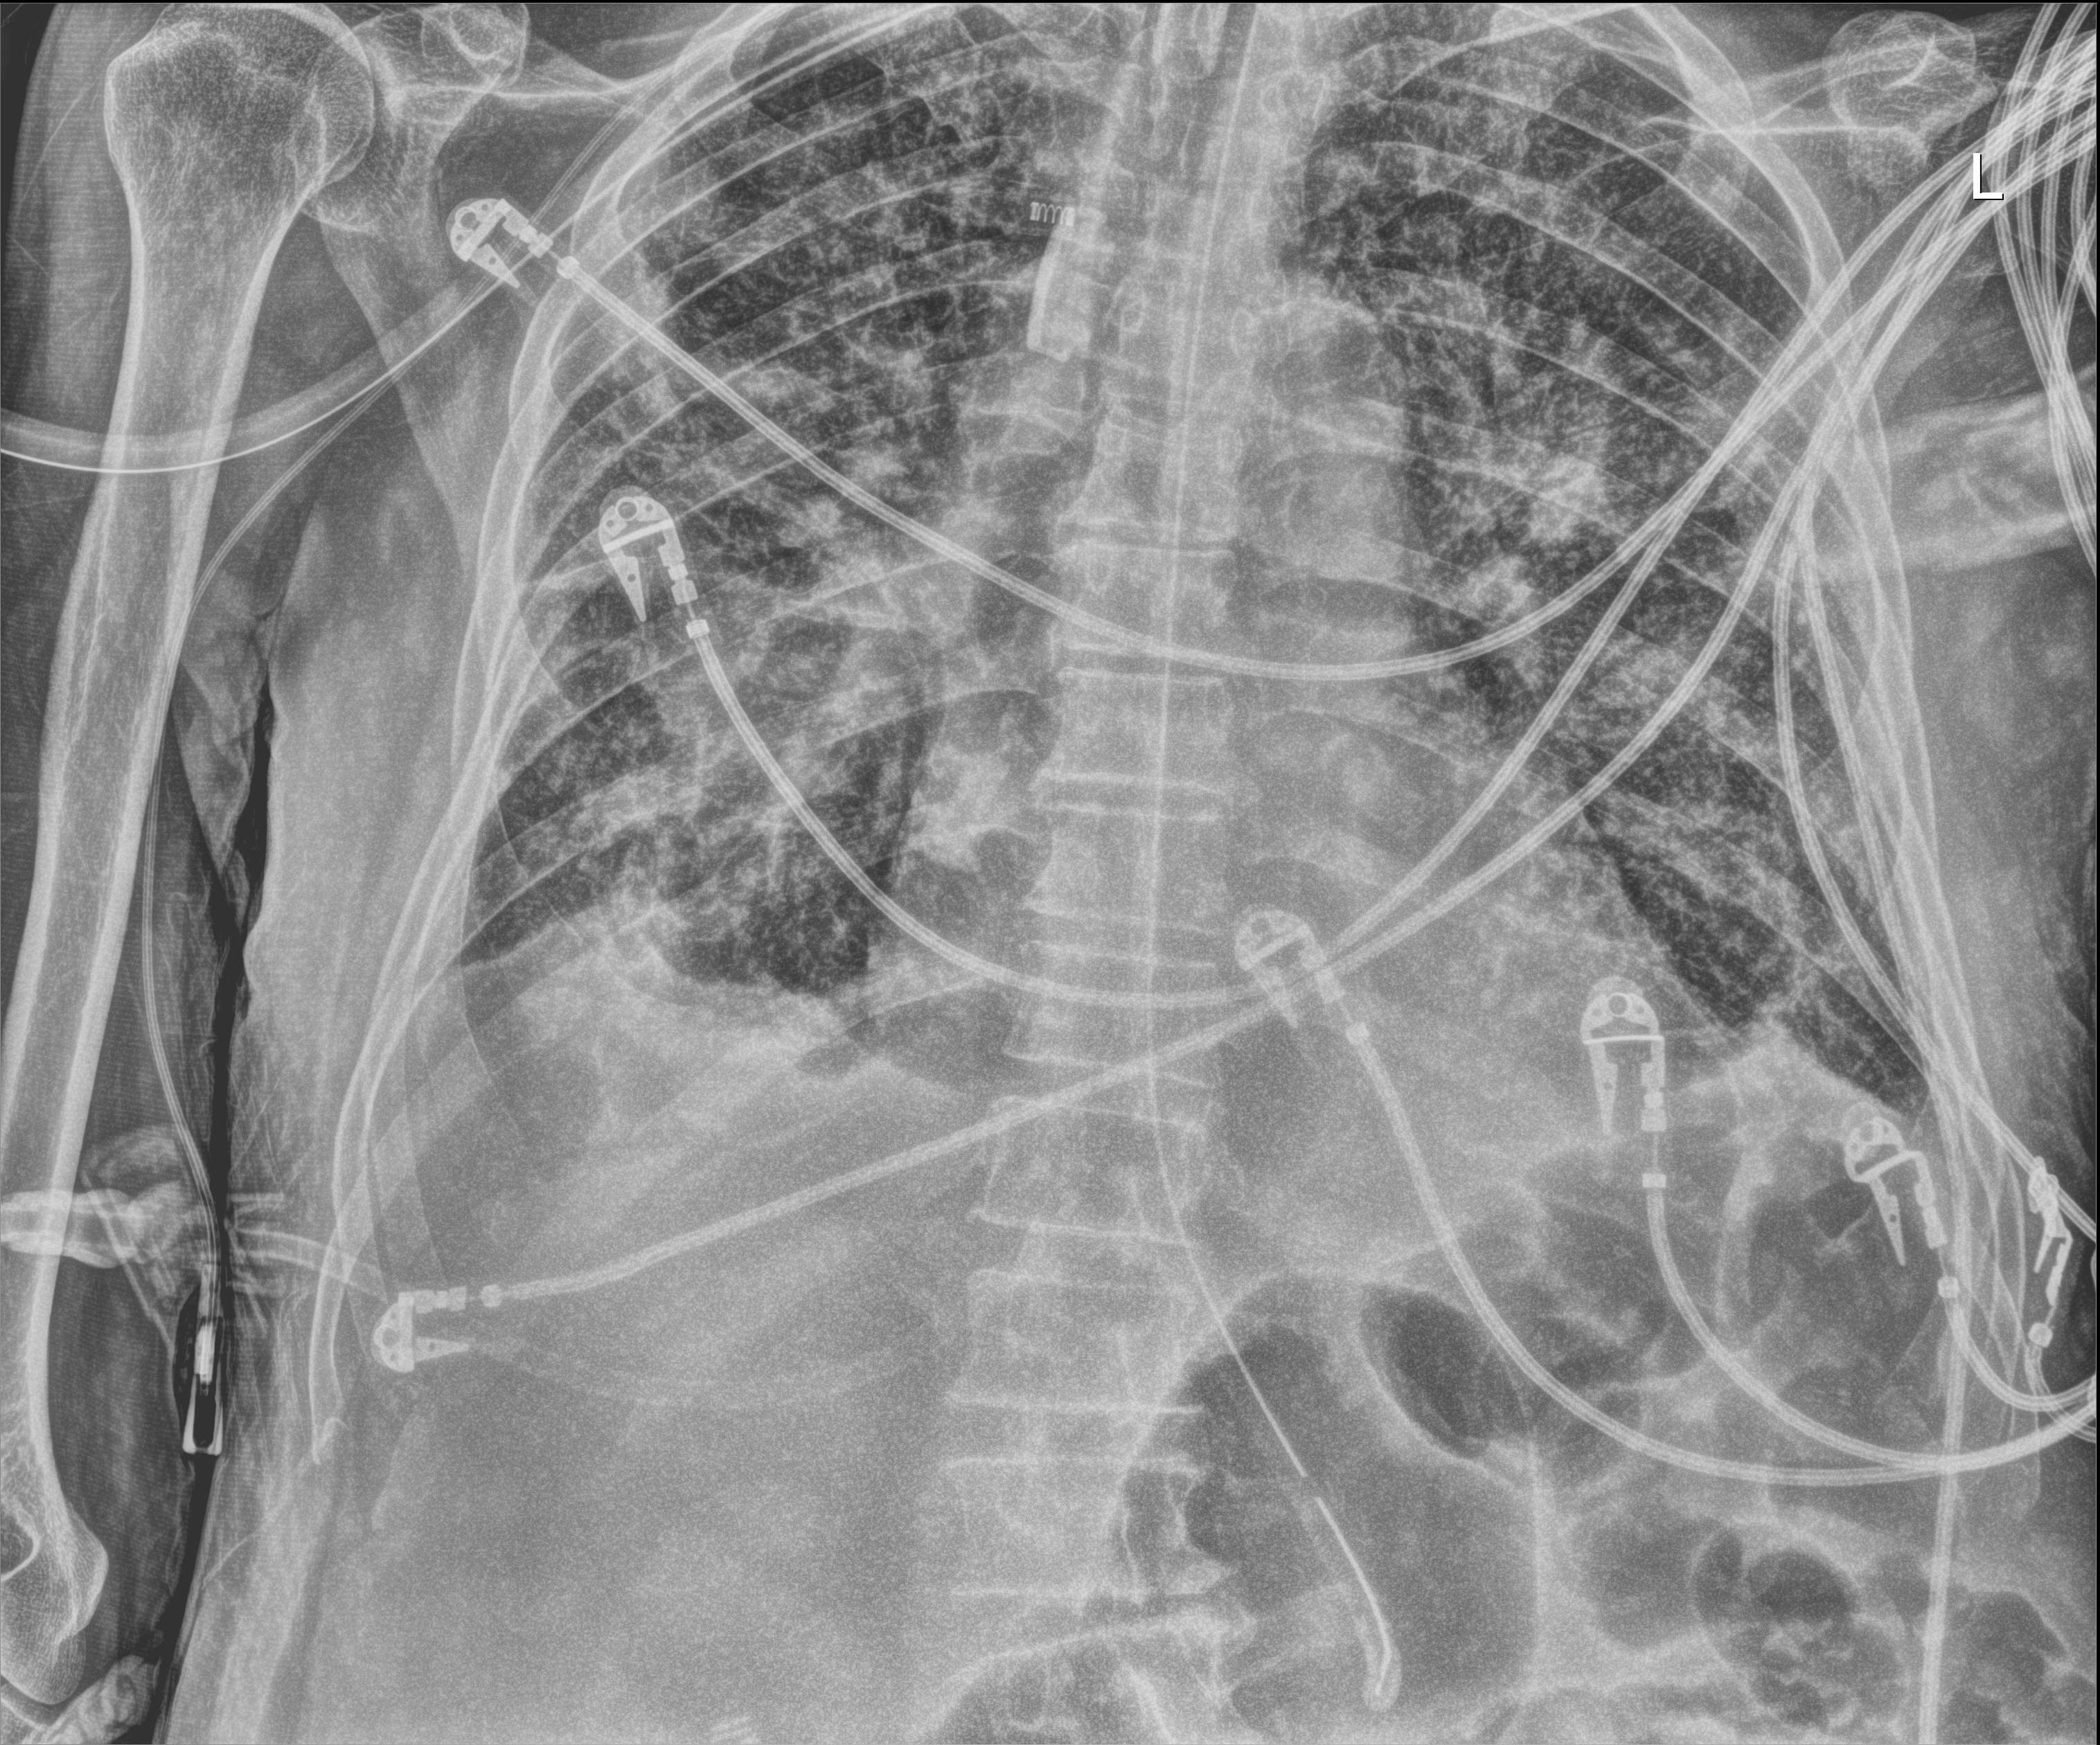
Bedside chest radiograph (digital radiography); anteroposterior (AP) projection. Patient hospitalised with COVID-19; male, aged 75–90 years.
From the hospital-stay record, not from the radiograph (when in the stay this image was taken is not recorded): admitted to intensive care during this hospital stay: yes; hypertension (admission record): no; diabetes (admission record): no.